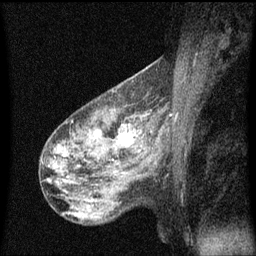
Breast MRI (dynamic contrast-enhanced), one sagittal slice; slice 38 of 60 in the series (ordered by position); dynamic contrast-enhanced series, image 2 of 3 at this slice position (ordered by acquisition); 1.5 T; TE 4.2 ms, TR 8 ms; 2 mm slice thickness; 256 × 256 image matrix, field of view 200 × 200 mm. Patient: female, 50 years.
Structures marked on this image (semi-automatic segmentation, software-assisted and operator-edited):
- analysis volume of interest (the breast-tissue region the enhancement analysis was run in; not a lesion): bounding box [x1, y1, x2, y2] px = [106, 118, 148, 159]
- tumour enhancement mask (voxels above the 70 % enhancement threshold inside the analysis volume of interest): [118, 124, 133, 145]